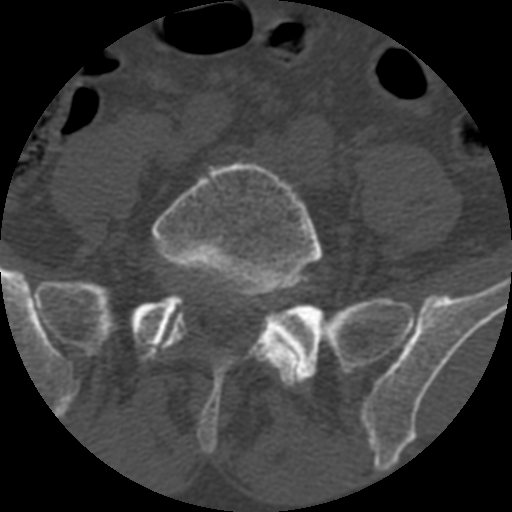
CT including the spine, one axial slice; position 248 of 399 along the scan axis; bone window (W 1800 / L 400 HU); 1.25 mm slice thickness; 512 × 512 image matrix, field of view 160 × 160 mm. Patient age 71 years. From the clinical record (not read from this slice): primary cancer: prostate.
Structures marked on this image (semi-automatically segmented with operator editing):
- L5 vertebra: box from (x=150, y=159) to (x=324, y=387) px